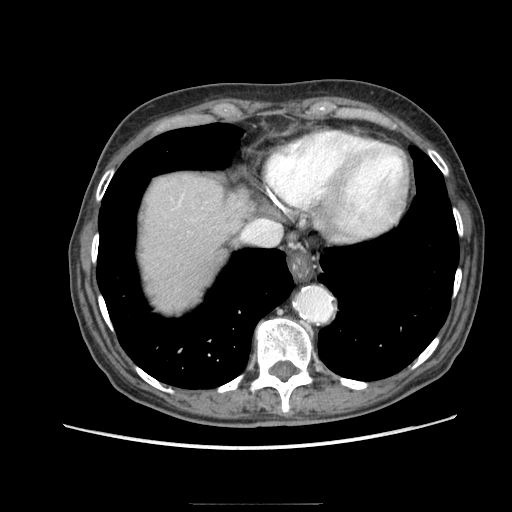
Contrast-enhanced abdominal CT (liver protocol), one axial slice; slice 74 of 83 in the series (ordered by position); 140 kVp; soft-tissue window (W 400 / L 40 HU); 2.5 mm slice thickness; 512 × 512 image matrix, field of view 360 × 360 mm. From the clinical record (not read from this slice): diagnosis: hepatocellular carcinoma (patient treated with transarterial chemoembolisation; whether this scan precedes or follows treatment is not stated here); TNM stage (as recorded): Stage-I; Child-Pugh class: A.
Annotated regions visible in this slice (semi-automatic segmentation, software-assisted and operator-edited):
- liver parenchyma outside the tumour (the mass and vessels are separate outlines, so this box may not span the whole liver): bounding box (x1, y1, x2, y2) in pixels: (140, 174, 252, 310)